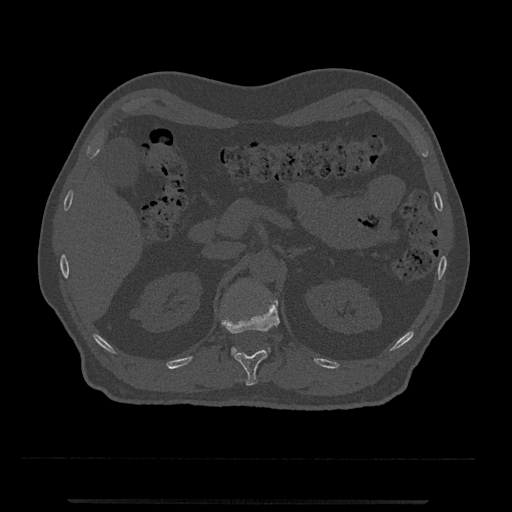
CT including the spine, one axial slice. Slice 378 of 797 in the series (ordered by position). 120 kVp. Bone window (W 1800 / L 400 HU). 512 × 512 image matrix. Male patient, age 63 years. From the clinical record (not read from this slice): primary cancer: prostate.
Annotated regions visible in this slice (semi-automatically segmented with operator editing):
- L1 vertebra: bounding box (x1, y1, x2, y2) in pixels: (231, 347, 271, 356)
- T12 vertebra: (222, 299, 280, 386)